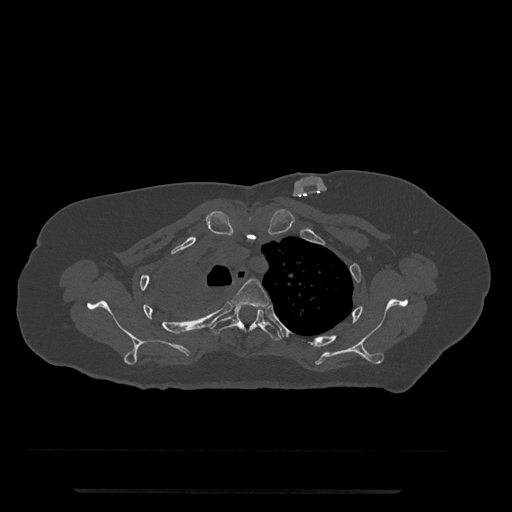
CT including the spine, one axial slice. Slice 607 of 797 in the series (ordered by position). Reconstruction kernel Br40s/3. 120 kVp. Bone window (W 1800 / L 400 HU). 0.5 mm slice thickness. 512 × 512 image matrix. Patient: female, 51 years. From the clinical record (not read from this slice): primary cancer: neuro.
Structures marked on this image (semi-automatic segmentation, software-assisted and operator-edited):
- T3 vertebra: bounding box <233,278,269,308> (left, top, right, bottom; pixels)
- T4 vertebra: <210,305,282,341>